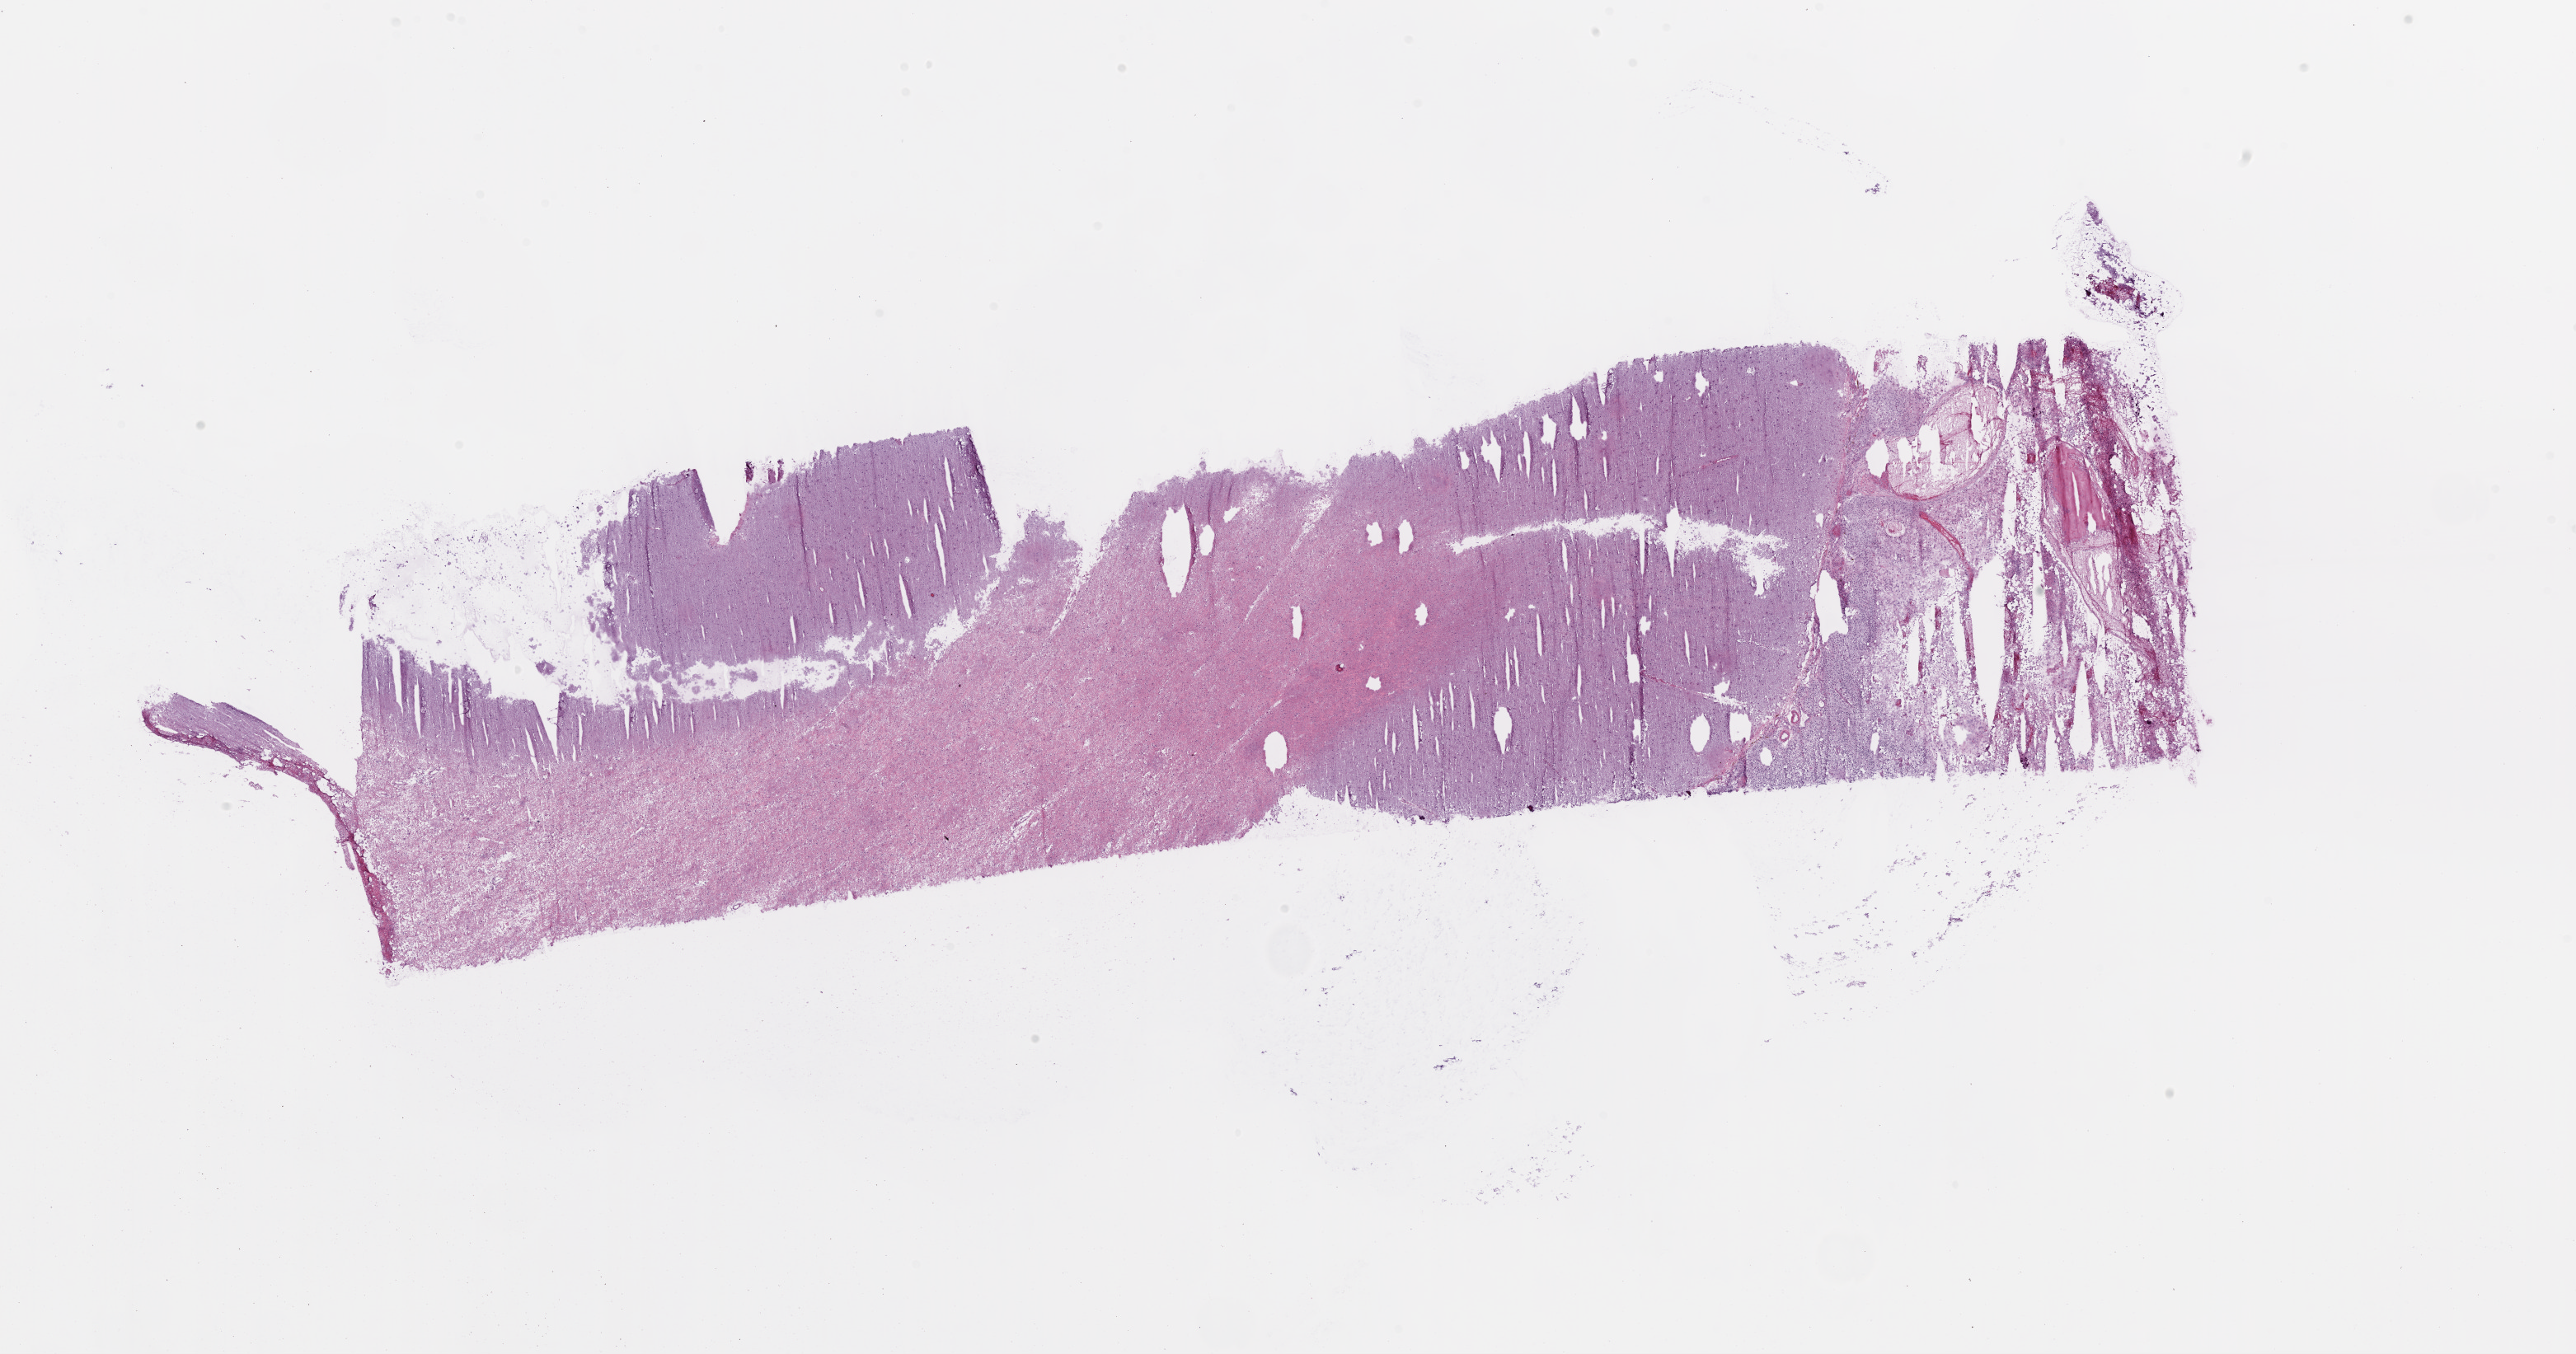
Whole-slide histology image, Hematoxylin and eosin (H&E) stained — a low-resolution overview of the entire scanned area, about 25.1 x 13.2 mm (slide scanned at 20x). Pathologist review of this section (percent, as recorded): tumour cells 30%, tumour nuclei 60%, normal cells 65%, stromal cells 0%, necrosis 5%.
Specimen: frozen section from the top of the tissue portion; brain, primary tumour sample.